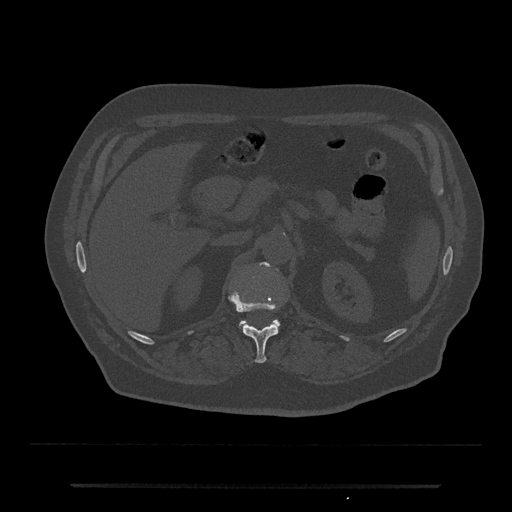
CT including the spine, one axial slice. Position 576 of 797 along the scan axis. Bone window (W 1800 / L 400 HU). 512 × 512 image matrix, field of view 434 × 434 mm. Patient: male, 80 years. Case-level facts recorded for this patient, not image findings: primary cancer: prostate; vertebrae with lytic lesions (as recorded): L1, T11.
Structures marked on this image (semi-automatically segmented with operator editing):
- L1 vertebra: bounding box <239,262,280,328> (left, top, right, bottom; pixels)
- T12 vertebra: <229,293,279,363>